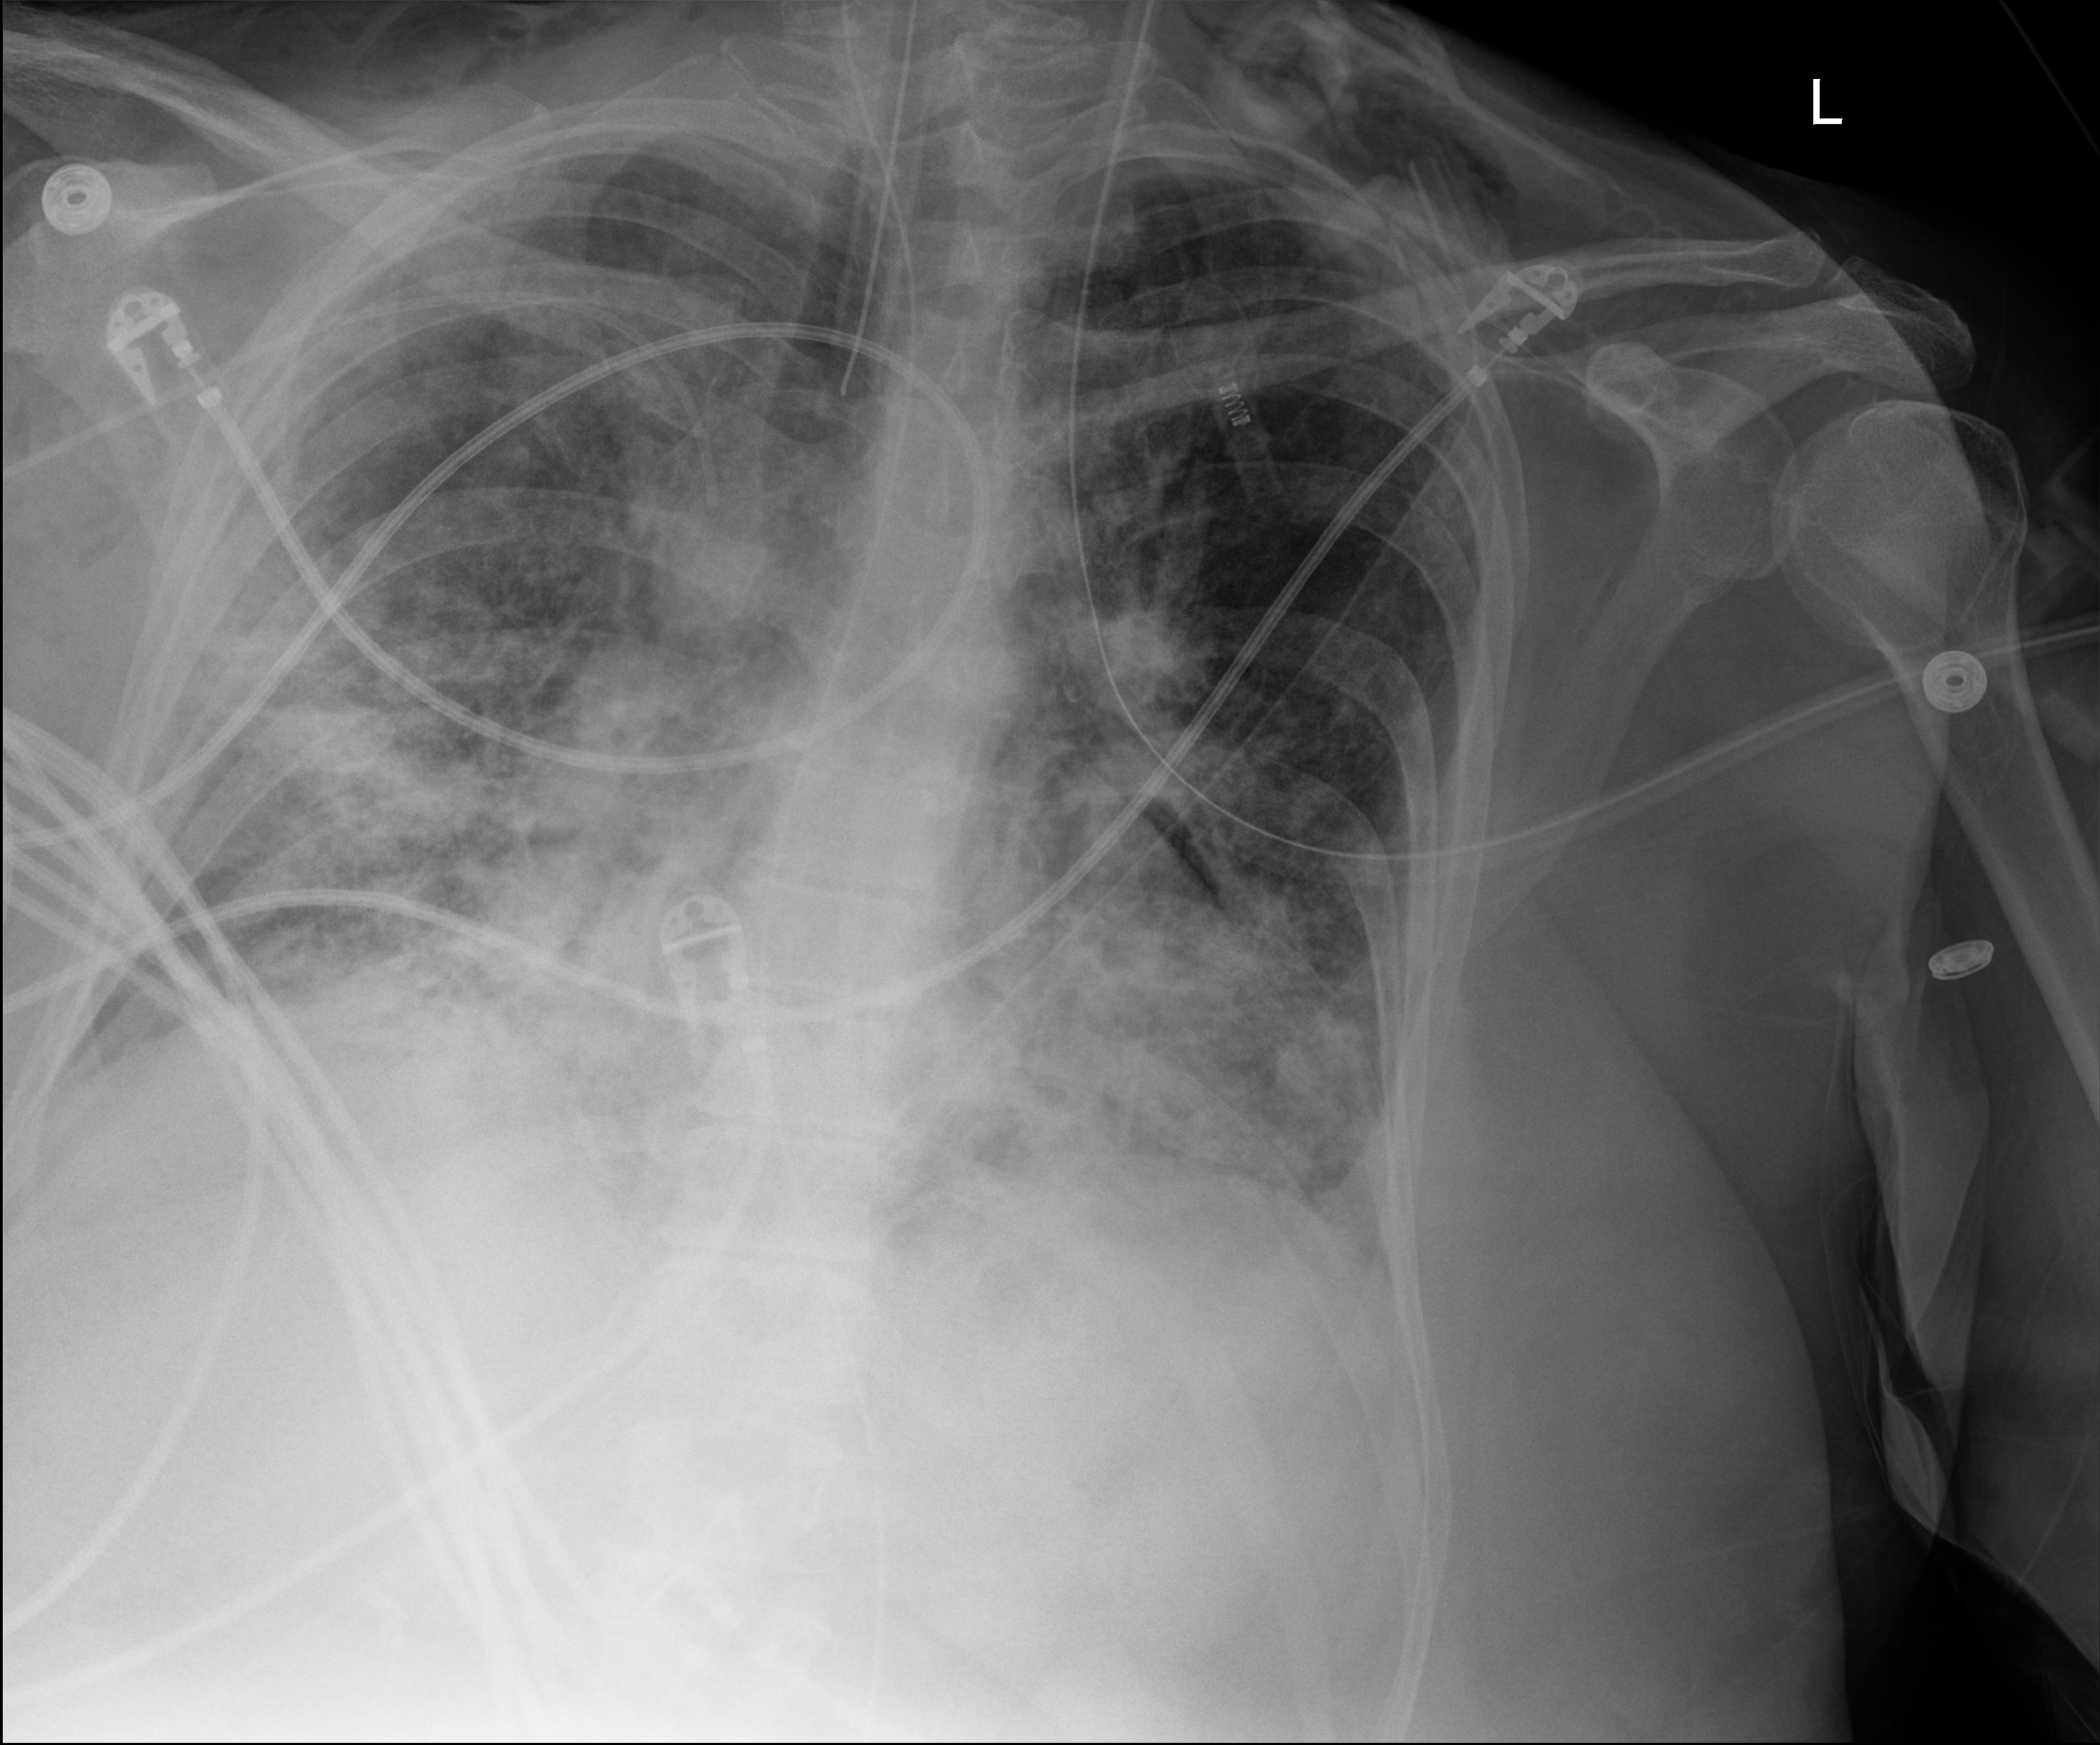
Chest X-ray (portable). Female patient hospitalised with COVID-19, age 60–74 years.
From the hospital-stay record, not from the radiograph (when in the stay this image was taken is not recorded):
- diabetes (admission record): no